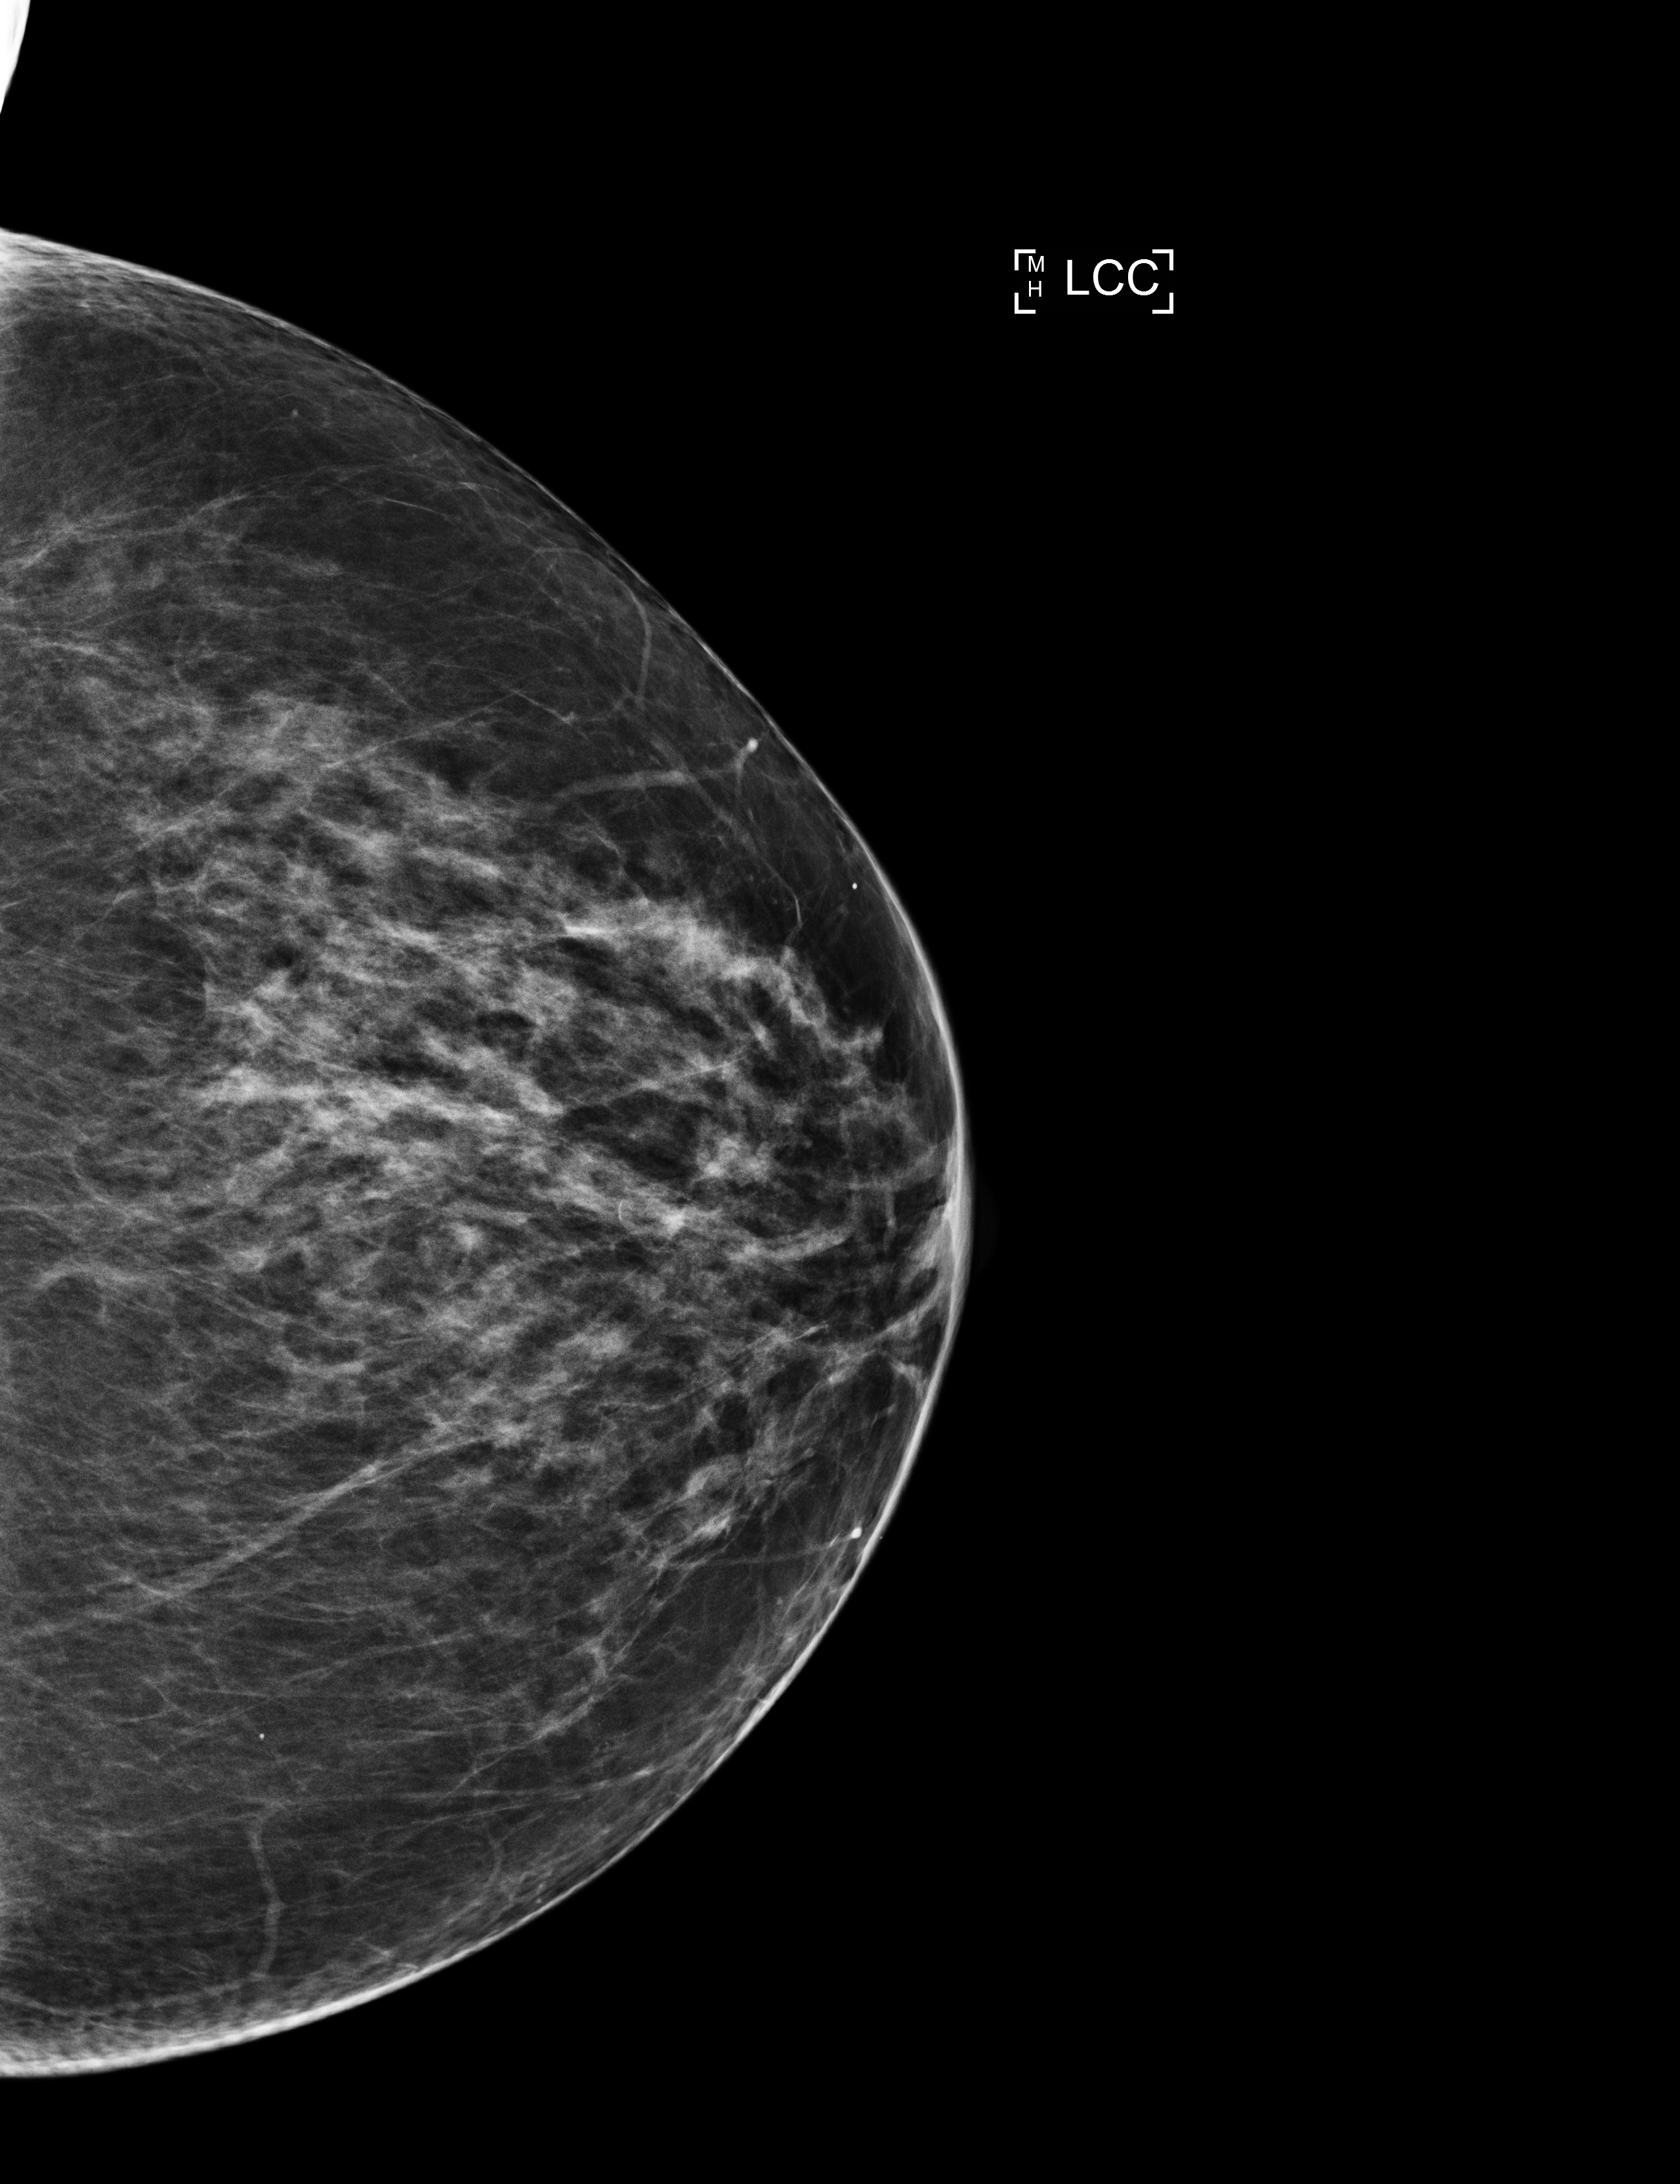
Screening examination; system: Selenia Dimensions. Patient aged 71 years (female).
Image type: full-field digital mammogram. Breast: left. Projection: cranio-caudal projection.